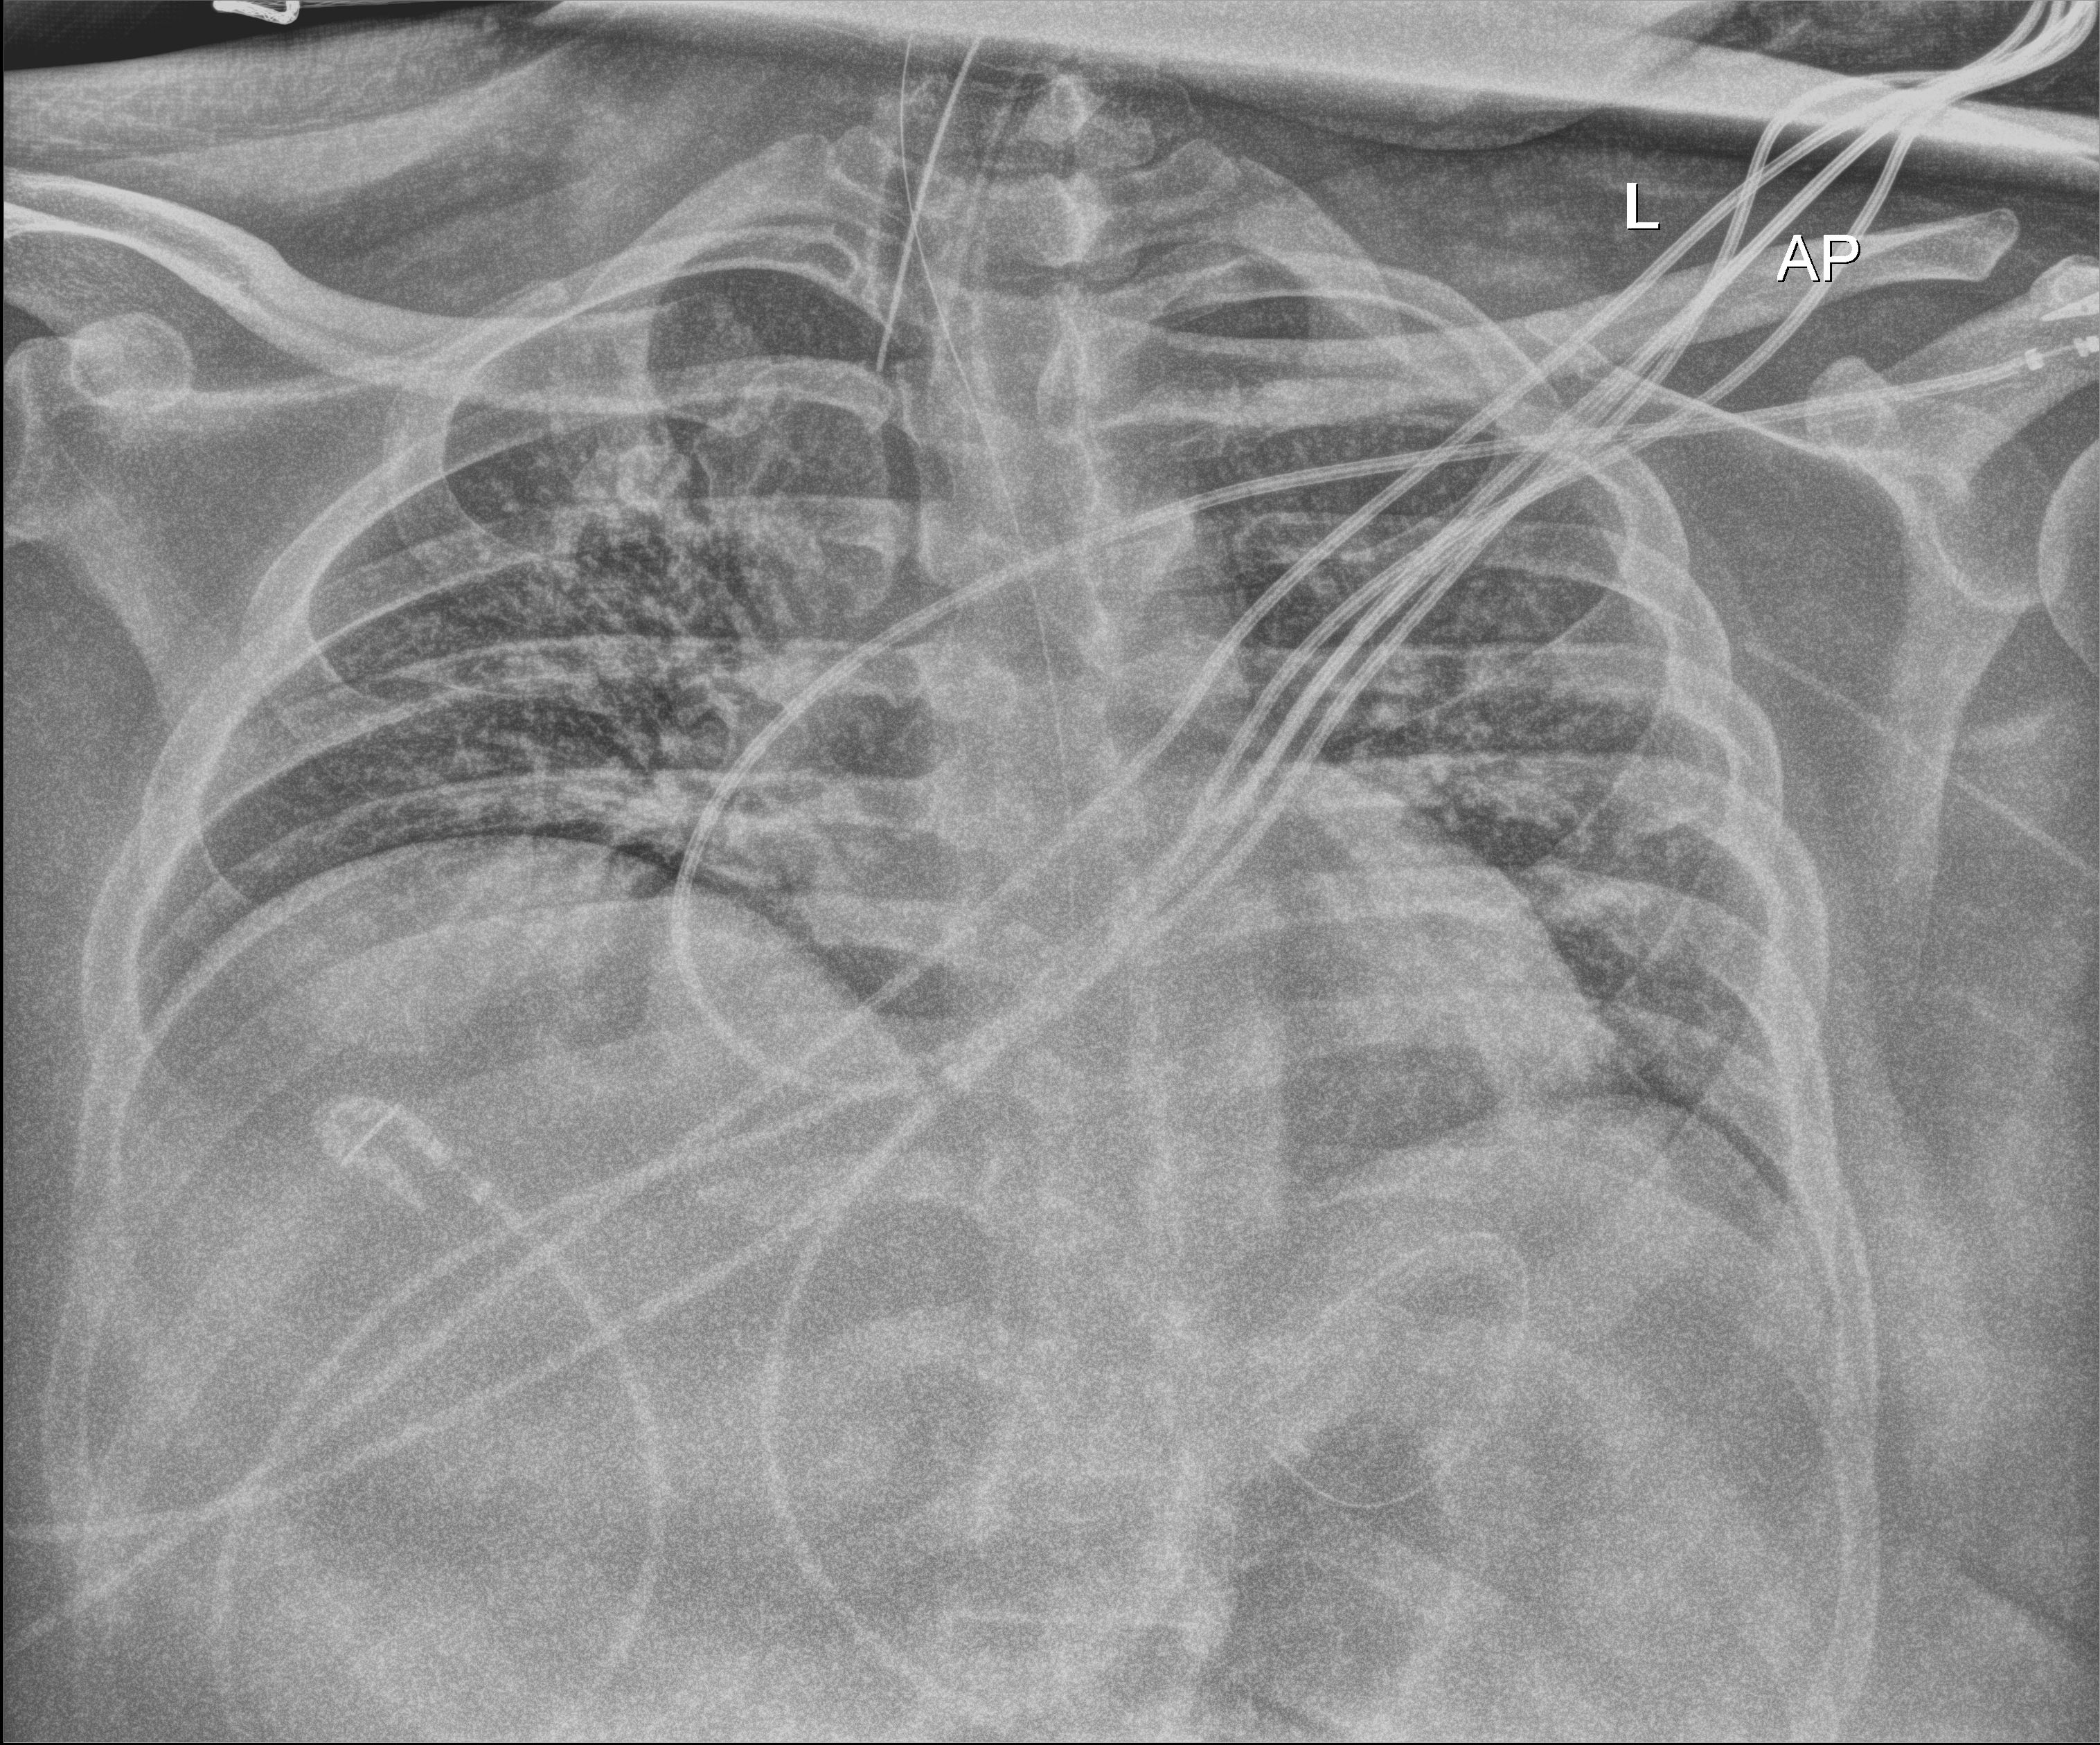
Chest X-ray (portable), anteroposterior (AP) projection. Patient hospitalised with COVID-19; male, aged 18–59 years.
Hospital-stay facts (about this admission, not read from this image; timing relative to this image not recorded): other chronic lung disease (admission record): yes; mechanically ventilated during this hospital stay: yes.